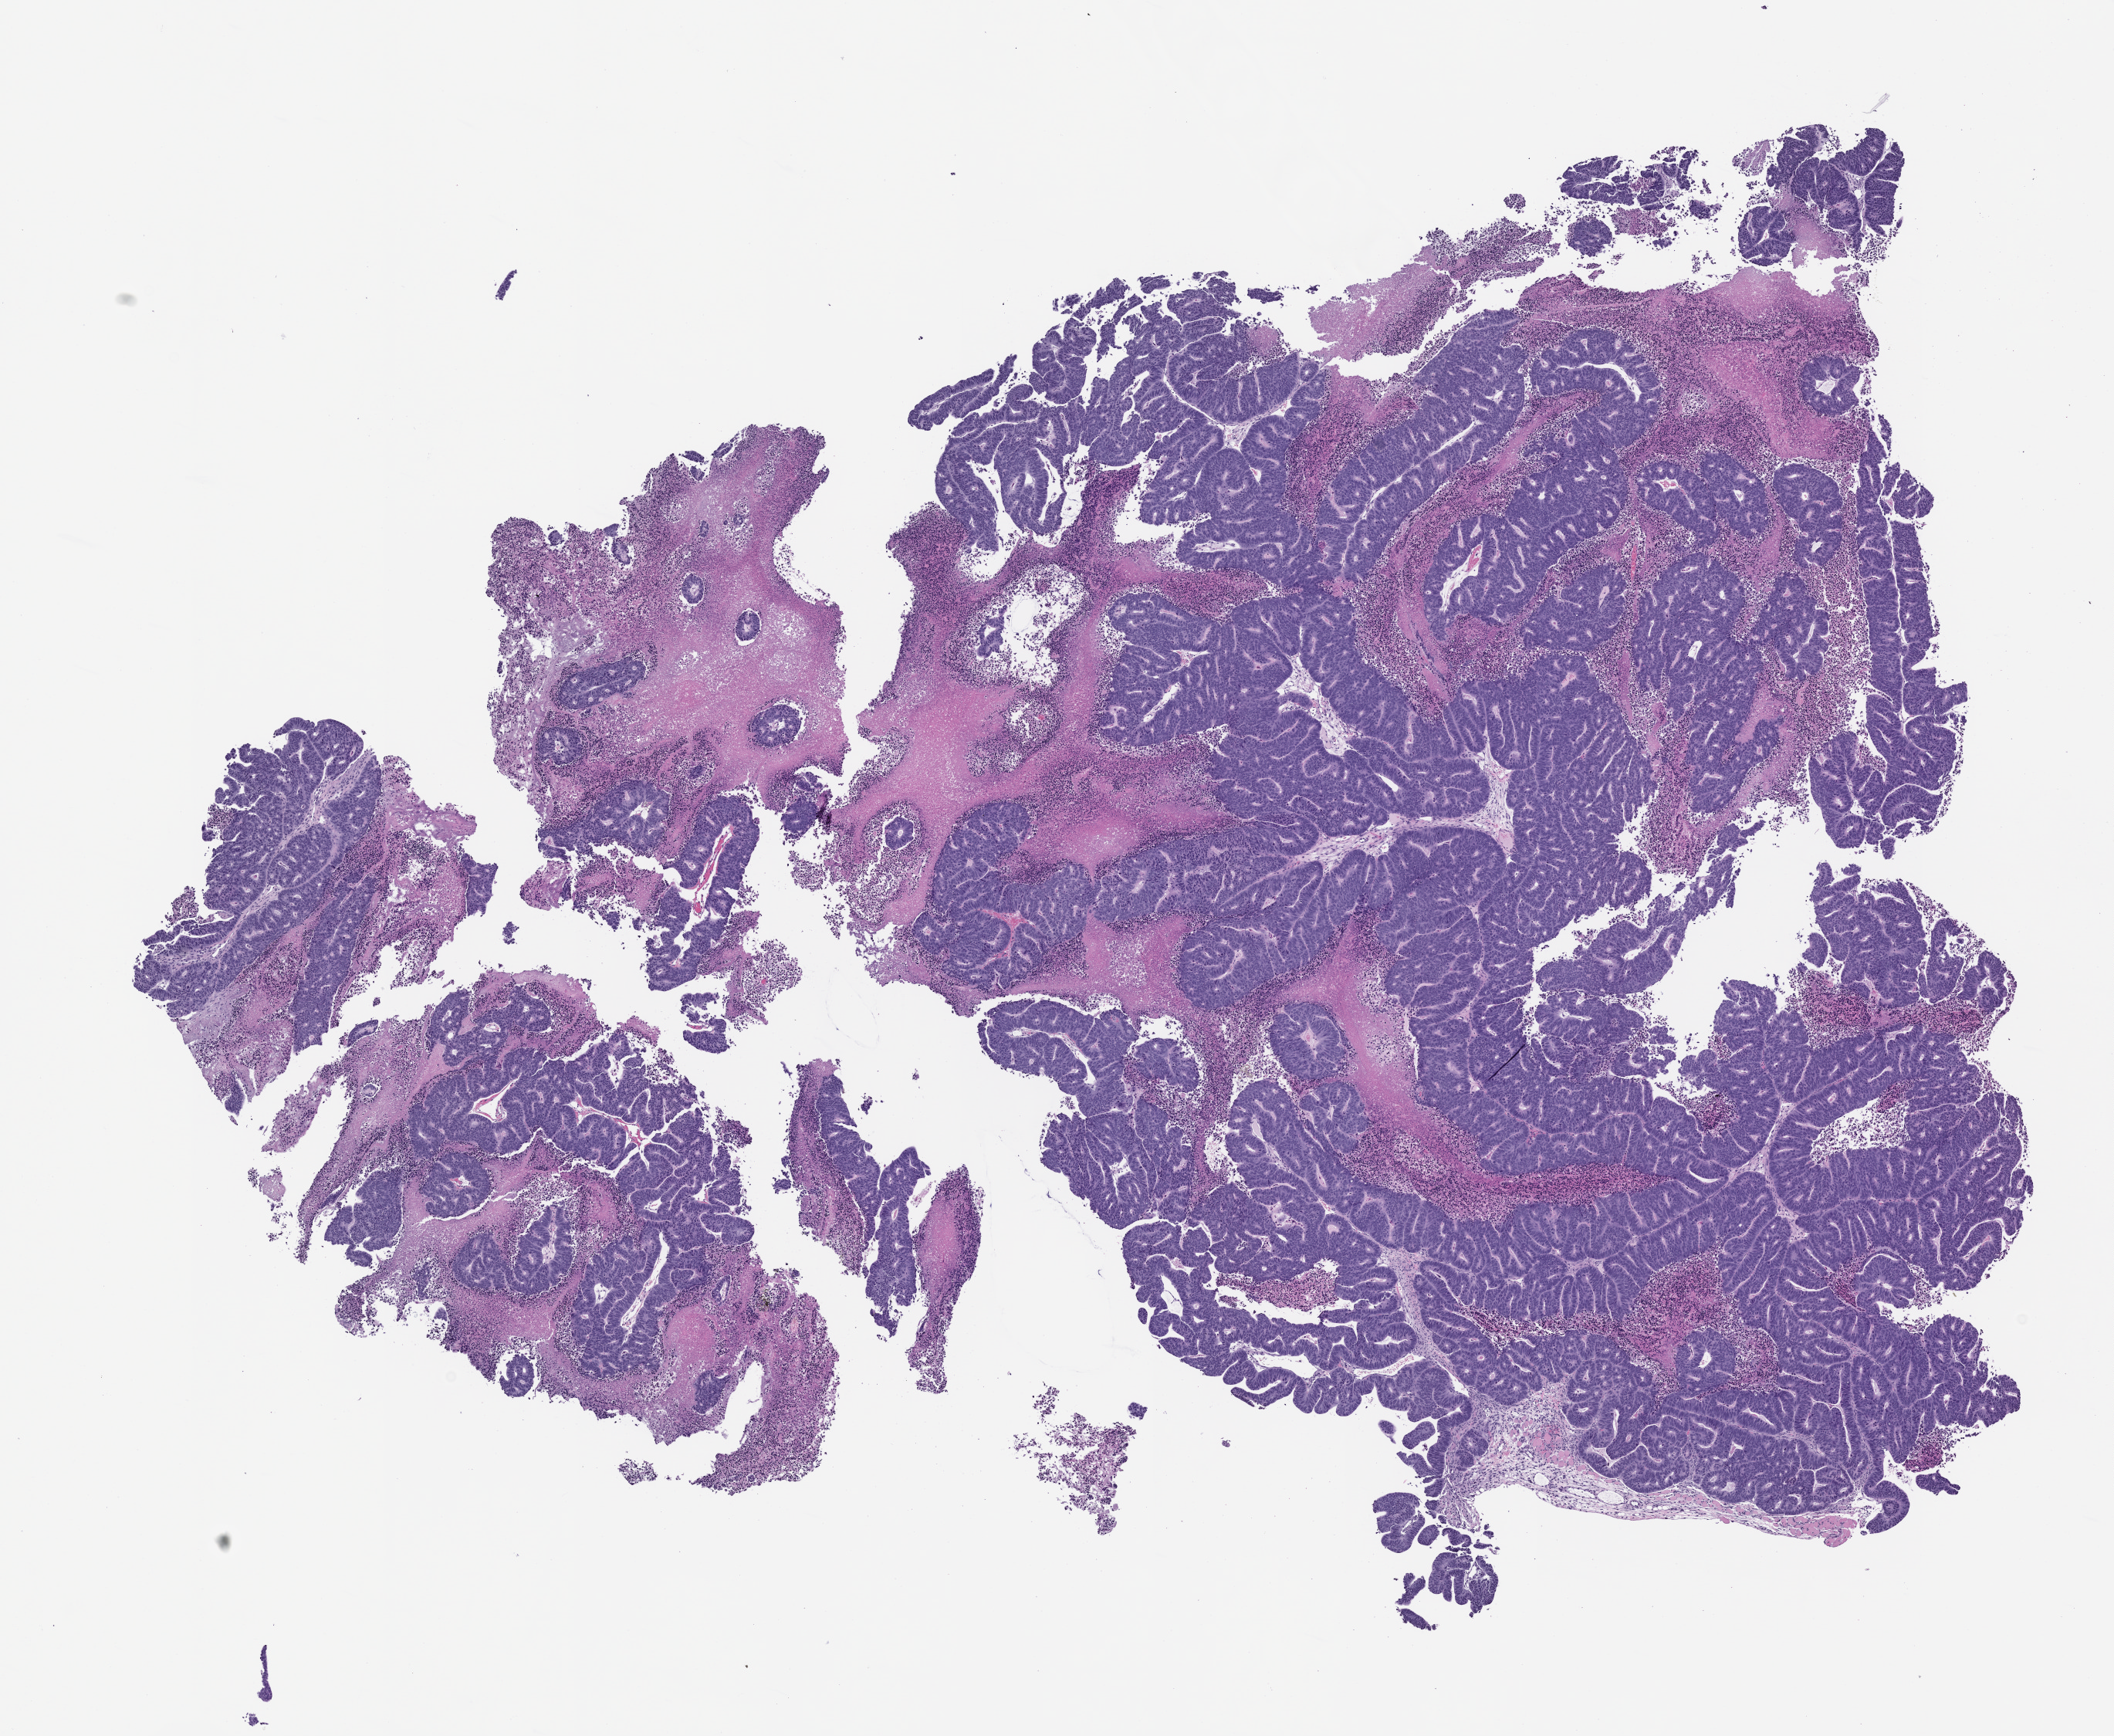
H&E whole-slide image of a patient-derived xenograft (PDX) tumor grown in a mouse, passage 1 — a low-resolution overview of the entire scanned area, about 11.0 x 9.0 mm; formalin-fixed paraffin-embedded section; originating tumor site category: colon.
Originating patient diagnosis: Colon Adenocarcinoma.